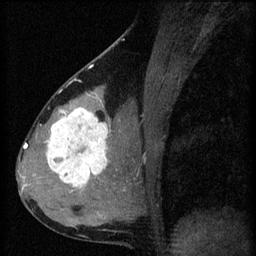
Breast MRI (dynamic contrast-enhanced), one sagittal slice. Position 31 of 60 along the scan axis. 3 images stored at this slice position (order not interpretable as contrast timing). 1.5 T. TE 4.2 ms, TR 8.2 ms. 256 × 256 image matrix, field of view 180 × 180 mm. Female patient, age 37 years.
Outlined on this slice (semi-automatic segmentation, software-assisted and operator-edited):
- analysis volume of interest (the breast-tissue region the enhancement analysis was run in; not a lesion): bounding box <44,100,119,197> (left, top, right, bottom; pixels)
- tumour enhancement mask (voxels above the 70 % enhancement threshold inside the analysis volume of interest): <47,108,112,187>